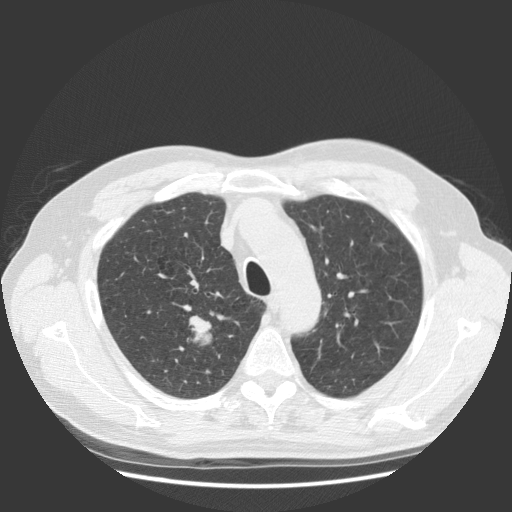
Low-dose screening chest CT, axial slice, baseline screening round, lung window (W 1500 / L -600 HU), slice 97 of 131 in the series. Male participant, aged 63 years at enrolment. Current smoker at enrolment.
Expert reader's lesion annotation, bounding box (x1, y1, x2, y2) in pixels: (156, 301, 228, 376). The screening reader recorded 2 non-calcified nodules or masses ≥4 mm on this exam; which of them this box marks is not recorded. Official screen result: positive, change unspecified: nodule(s) >= 4 mm or enlarging nodule(s), mass(es), or other non-specific abnormalities suspicious for lung cancer. Later outcome: lung cancer diagnosed 30 days after this screen — squamous cell carcinoma, NOS, right upper lobe, stage IIIB (AJCC 6th edition), 35 mm at pathology.